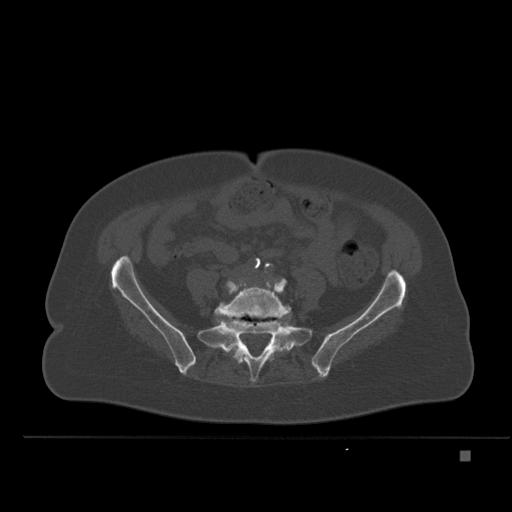
CT including the spine, one axial slice; slice 154 of 477 in the series (ordered by position); bone window (W 1800 / L 400 HU); 512 × 512 image matrix. Patient: female, 74 years. From the clinical record (not read from this slice): primary cancer: colon.
Annotated regions visible in this slice (semi-automatically segmented with operator editing):
- L5 vertebra: bounding box [x1, y1, x2, y2] px = [214, 279, 291, 360]